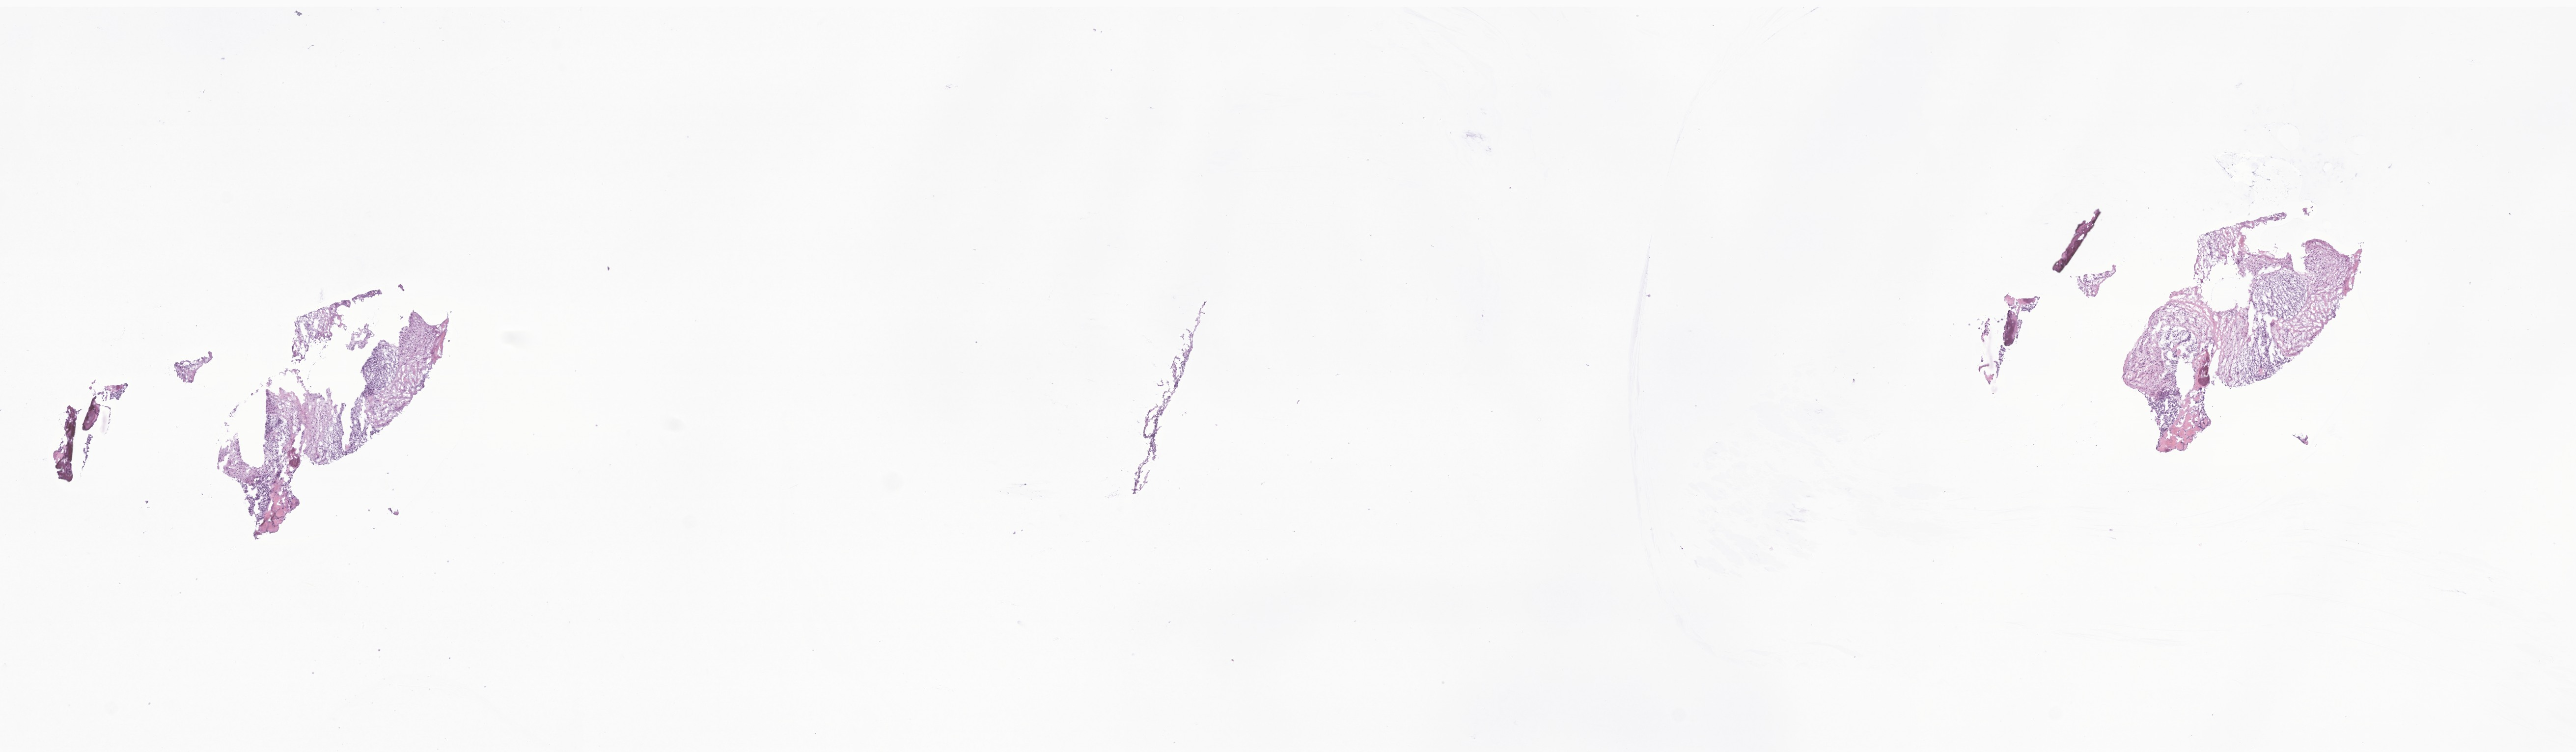
Digitized haematoxylin and eosin-stained section of tumor tissue from the long bone of lower limb — low-resolution overview of the scanned area, about 22.1 x 6.5 mm. Frozen section (OCT-embedded). Female patient, age 136 months (11 years 4 months).
* tissue or organ of origin (case record): long bones of lower limb and associated joints
* diagnosis: Ossifying fibromyxoid tumor, NOS